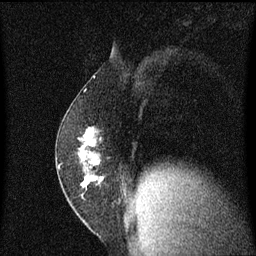
Breast MRI (dynamic contrast-enhanced), one sagittal slice. Slice 33 of 60 in the series (ordered by position). Dynamic contrast-enhanced series, image 2 of 3 at this slice position (ordered by acquisition). 1.5 T. TE 4.2 ms, TR 8.4 ms. 2 mm slice thickness. 256 × 256 image matrix, field of view 200 × 200 mm. Female patient, age 52 years. From the clinical record (not read from this slice): setting: breast cancer imaged before/during neoadjuvant chemotherapy; receptor status: HER2-positive.
Annotated regions visible in this slice (semi-automatically segmented with operator editing):
- analysis volume of interest (the breast-tissue region the enhancement analysis was run in; not a lesion): box from (x=57, y=124) to (x=108, y=191) px
- tumour enhancement mask (voxels above the 70 % enhancement threshold inside the analysis volume of interest): (x=82, y=128)–(x=95, y=187)